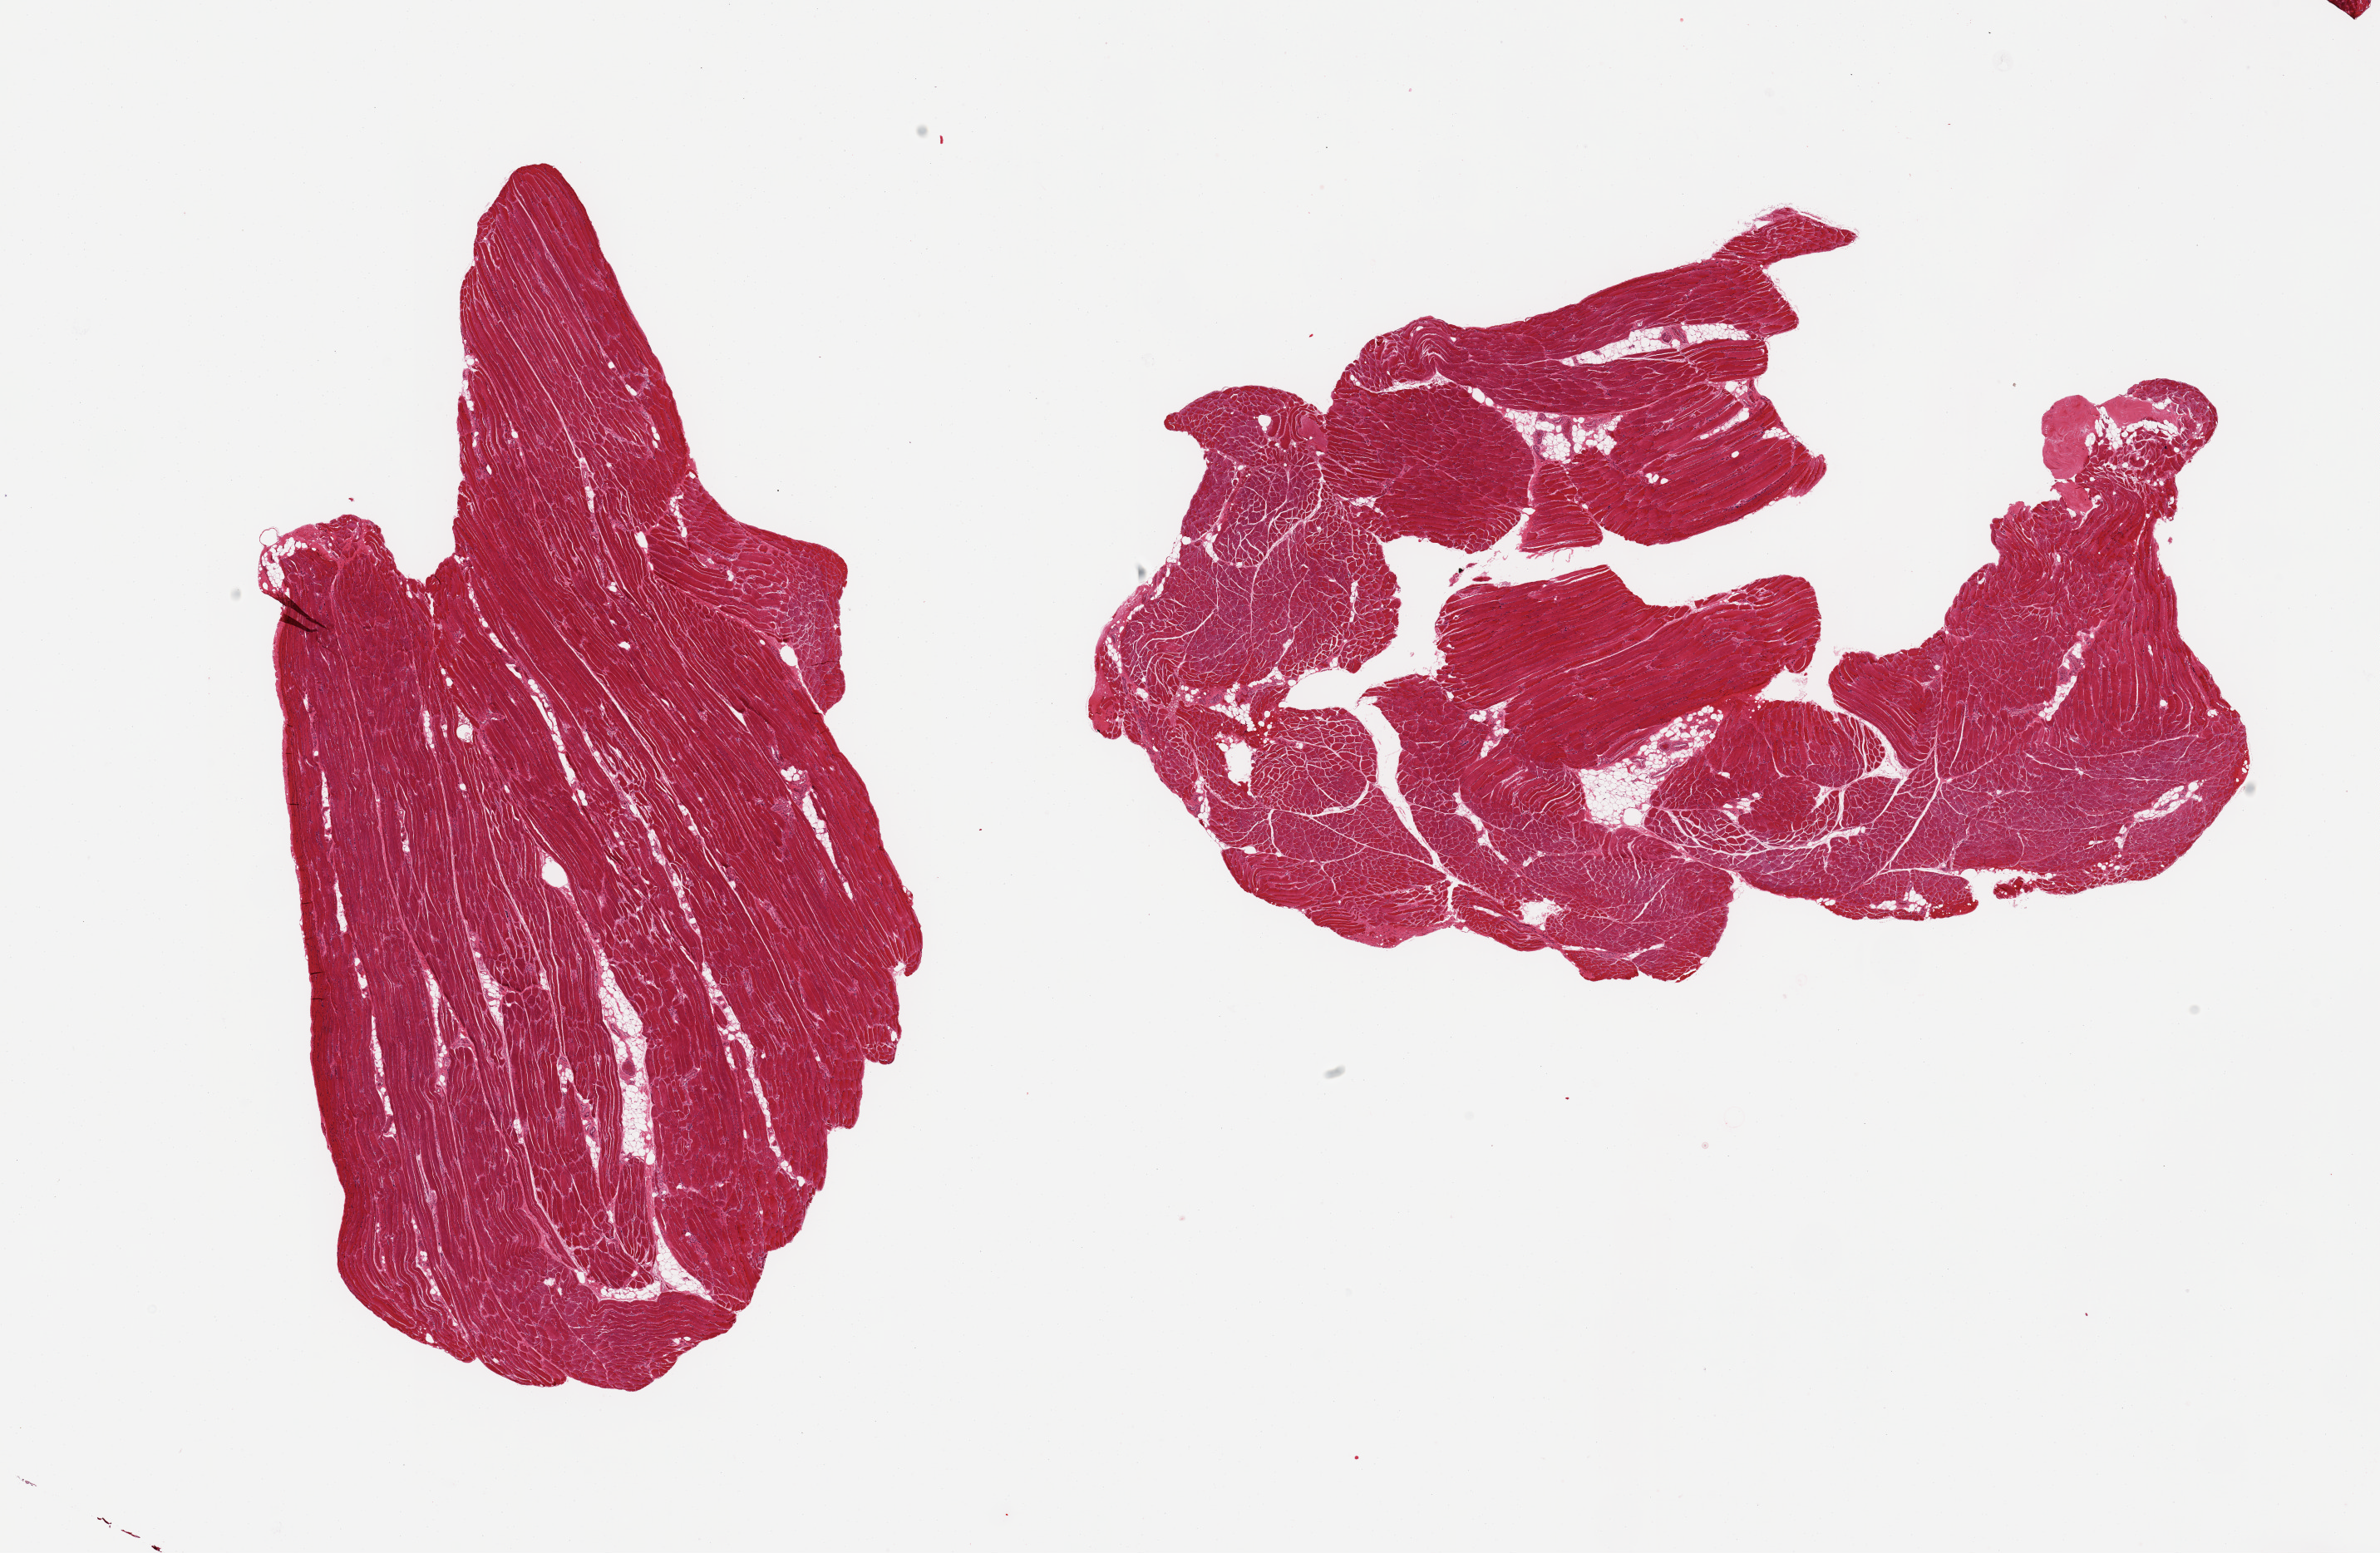
Digitized haematoxylin and eosin-stained section — a low-resolution overview of the entire scanned area, about 22.6 x 14.8 mm (from a 20x scan), PAXgene-fixed, paraffin-embedded tissue, section of skeletal muscle (target tissue), tissue donor sample. Donor: female.
- review note (as recorded): 2 pieces